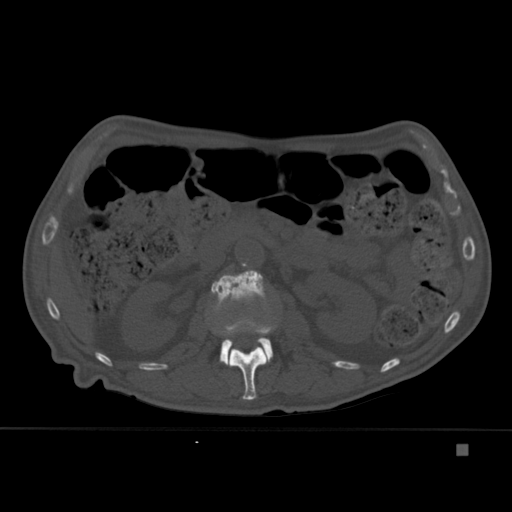
CT including the spine, one axial slice. Position 174 of 451 along the scan axis. Bone window (W 1800 / L 400 HU). 1.5 mm slice thickness. 512 × 512 image matrix, field of view 378 × 378 mm. Patient: male, 75 years. Case-level facts recorded for this patient, not image findings: primary cancer: prostate.
Annotated regions visible in this slice (semi-automatically segmented with operator editing):
- L1 vertebra: bounding box [x1, y1, x2, y2] px = [222, 321, 274, 400]
- L2 vertebra: [211, 270, 274, 365]